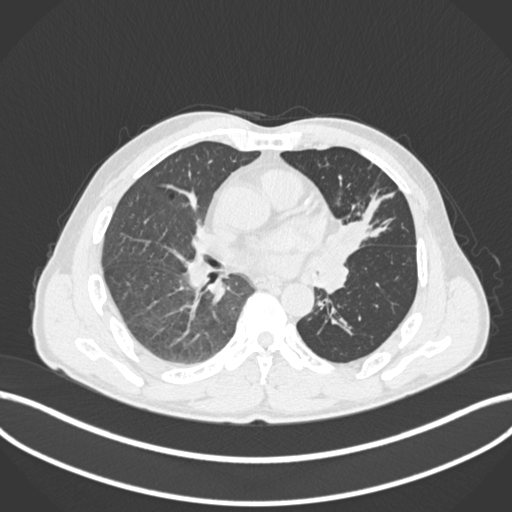
Chest CT, one axial slice. Position 93 of 255 along the scan axis. 120 kVp. Lung window (W 1500 / L -600 HU). 1 mm slice thickness. 512 × 512 image matrix. Patient: male, 57 years. From the clinical record (not read from this slice): clinical TNM (as recorded): T2b N0 M0.
Structures marked on this image (rectangle marked by the reading radiologist):
- lung tumour (recorded histology: squamous cell carcinoma): bounding box [x1, y1, x2, y2] px = [324, 210, 365, 275]